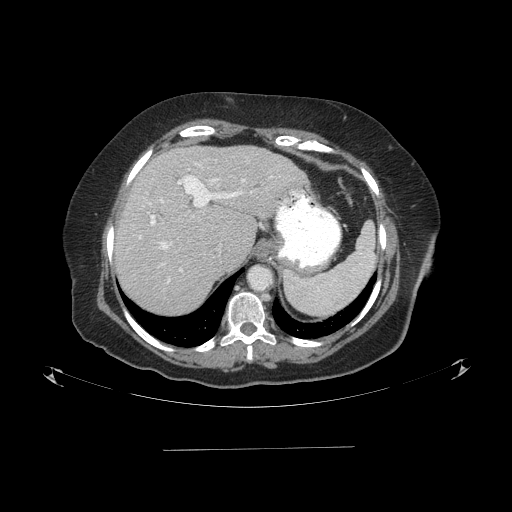
Contrast-enhanced abdominal CT (liver protocol), one axial slice; position 67 of 103 along the scan axis; one of 2 acquisitions stored at this slice position; soft-tissue window (W 400 / L 40 HU); 2.5 mm slice thickness; 512 × 512 image matrix, field of view 500 × 500 mm. Case-level facts recorded for this patient, not image findings: diagnosis: hepatocellular carcinoma (patient treated with transarterial chemoembolisation; whether this scan precedes or follows treatment is not stated here); TNM stage (as recorded): Stage-IIIA; Child-Pugh class: A; tumour differentiation: poorly differentiated.
Structures marked on this image (semi-automatically segmented with operator editing):
- abdominal aorta: bounding box <248,266,272,290> (left, top, right, bottom; pixels)
- liver parenchyma outside the tumour (the mass and vessels are separate outlines, so this box may not span the whole liver): <114,146,308,314>
- liver vessels: <139,164,273,283>